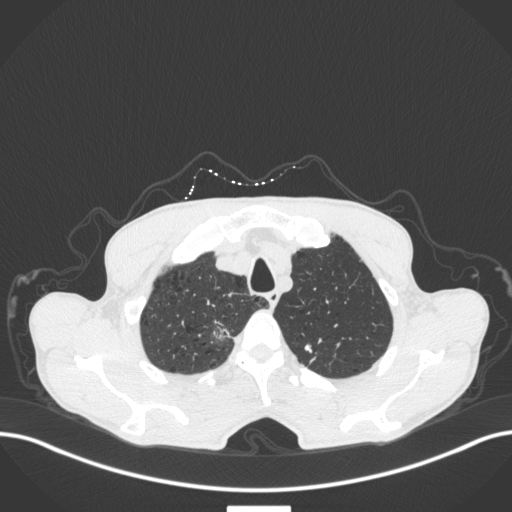
Chest CT, one axial slice. Position 370 of 445 along the scan axis. 120 kVp. Lung window (W 1500 / L -600 HU). 512 × 512 image matrix. Male patient, age 70 years. From the clinical record (not read from this slice): clinical TNM (as recorded): T1a N0 M0.
Structures marked on this image (rectangle marked by the reading radiologist):
- lung tumour (recorded histology: adenocarcinoma): bounding box [x1, y1, x2, y2] px = [206, 318, 233, 343]